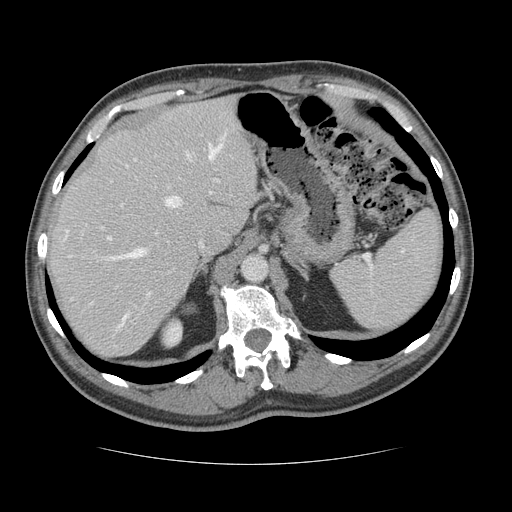
Contrast-enhanced abdominal CT, one axial slice. Slice 93 of 134 in the series (ordered by position). Reconstruction kernel STANDARD. Intravenous contrast given. Soft-tissue window (W 400 / L 40 HU). 512 × 512 image matrix. Male patient, age 68 years. Case-level facts recorded for this patient, not image findings: diagnosis: colorectal cancer liver metastases, imaged before liver resection; multiple liver metastases: yes; largest metastasis: 2.2 cm; disease in both lobes: no.
Outlined on this slice (outlined manually by an expert reader):
- hepatic veins: box from (x=106, y=132) to (x=226, y=329) px
- liver: (x=47, y=98)–(x=259, y=359)
- planned liver remnant (the part of the liver to remain after resection): (x=47, y=98)–(x=259, y=334)
- portal vein (with intrahepatic branches): (x=107, y=142)–(x=220, y=296)